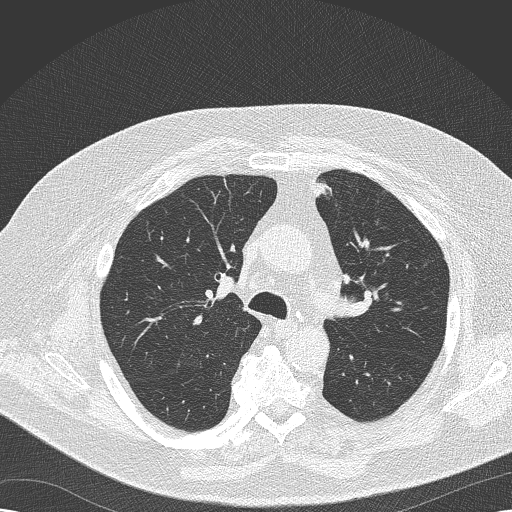
Axial slice from a low-dose chest CT screening exam, second annual screen, lung window (W 1500 / L -600 HU), 2 mm slice thickness, 512 × 512 image matrix, field of view 370 × 370 mm. Male participant, aged 68 years at enrolment. Former smoker at enrolment.
• Expert-annotated lung lesion, bounding box <322,269,373,335> (left, top, right, bottom; pixels).
• Screening reader's record for this exam (one nodule recorded; not confirmed to be the boxed lesion): non-calcified nodule or mass ≥4 mm, left lower lobe, 8 × 6 mm, soft tissue attenuation, pre-existing on the prior screen: yes; interval growth: no.
• Participant outcome: lung cancer diagnosed 256 days after this screen — squamous cell carcinoma, NOS, left upper lobe, poorly differentiated (G3), stage IIB (AJCC 6th edition), 35 mm at pathology.